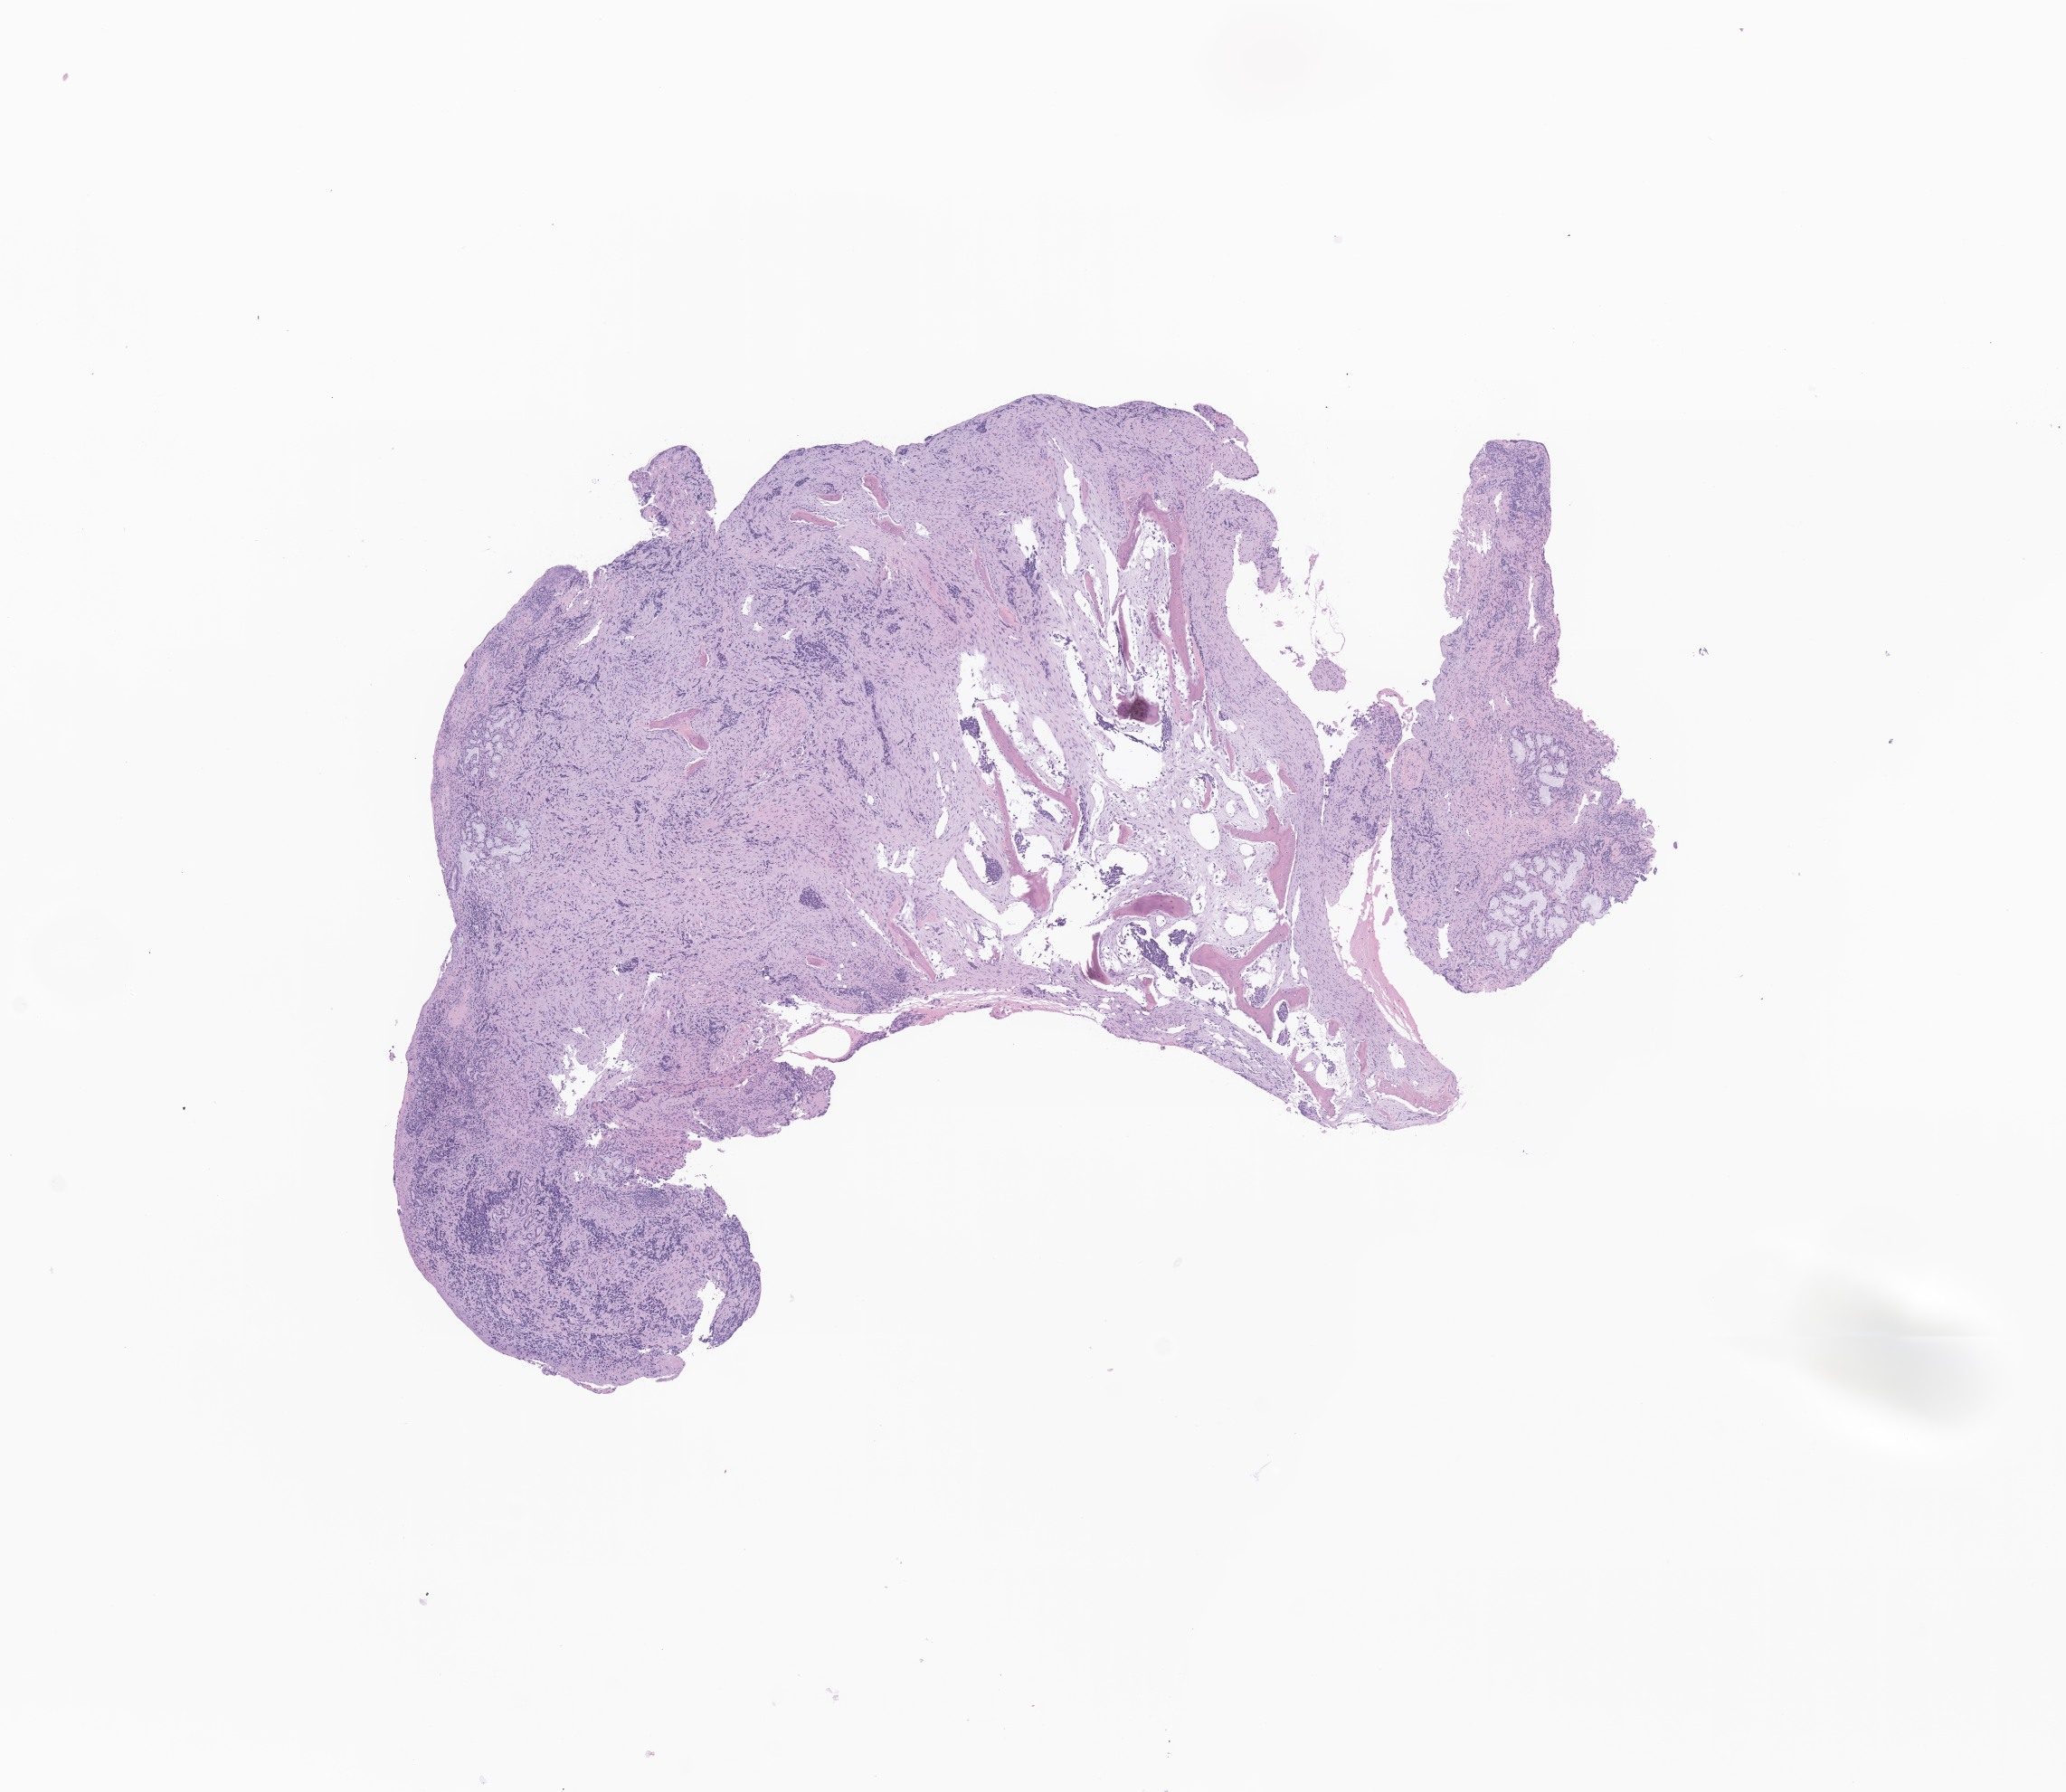
Digitized haematoxylin and eosin-stained section of tumor tissue from the ethmoid sinus — whole scanned area (about 9.6 x 8.4 mm) shown as a low-resolution overview; formalin-fixed, paraffin-embedded (FFPE) tissue. Patient: male, age 154 months (12 years 10 months).
Recorded diagnosis: Rhabdomyosarcoma, NOS.